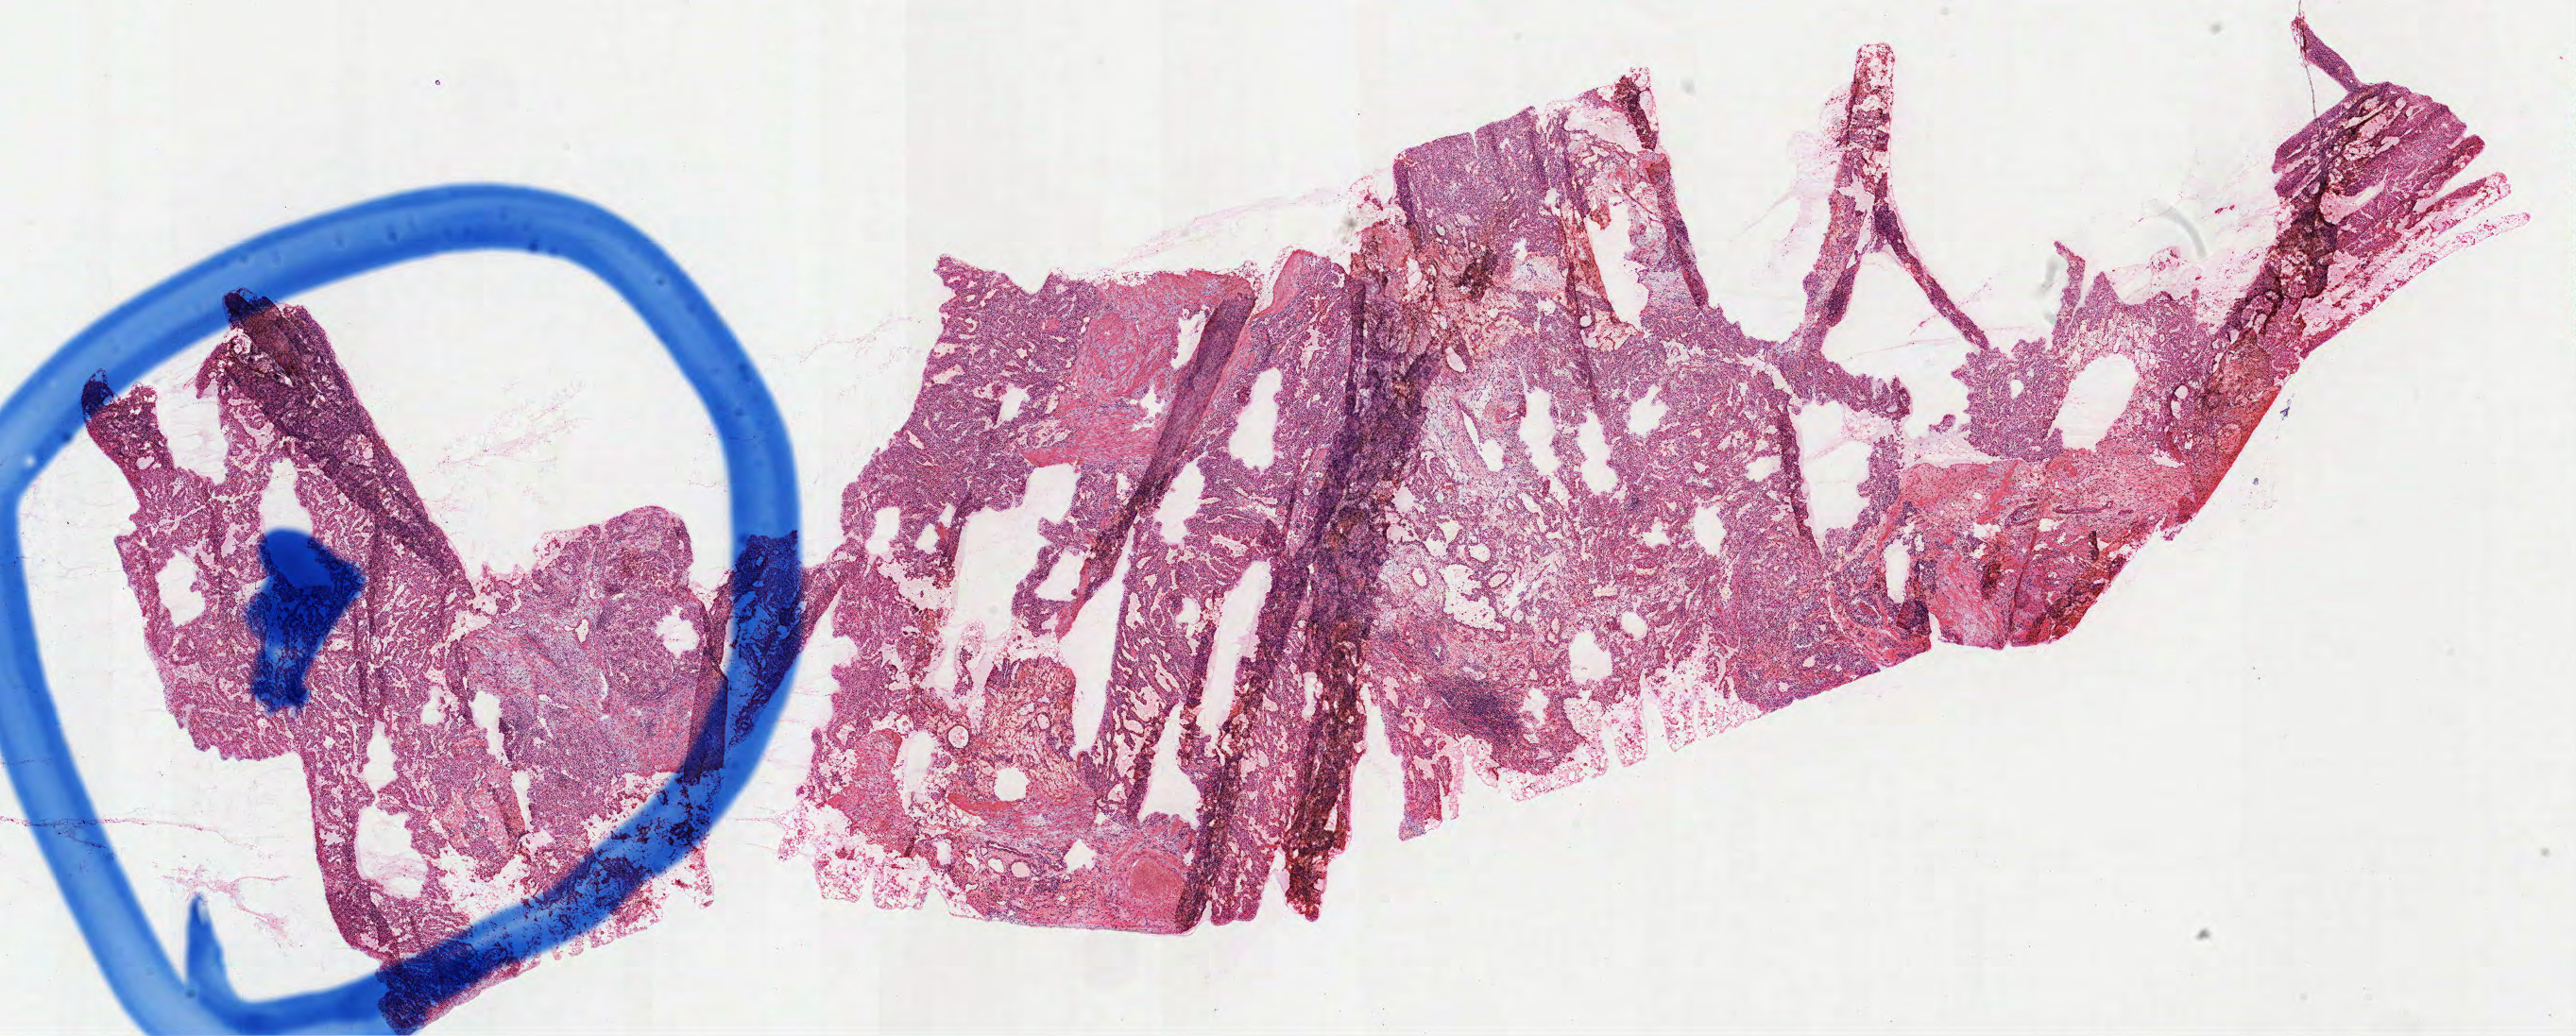
H&E-stained whole-slide image, low-resolution overview of the scanned area, about 22.0 x 8.8 mm (from a 40x scan); frozen section from the top of the tissue portion; sample: primary tumour, kidney. Male, age 54 years at initial diagnosis. Histologic grade: G3 (poorly differentiated). Pathologist review of this section (percent, as recorded): tumour cells 85%, tumour nuclei 78%, normal cells 0%, stromal cells 15%, necrosis 0%.
Pathologic diagnosis: Clear cell adenocarcinoma, NOS. AJCC pathologic stage: I (7th edition). Laterality: right.